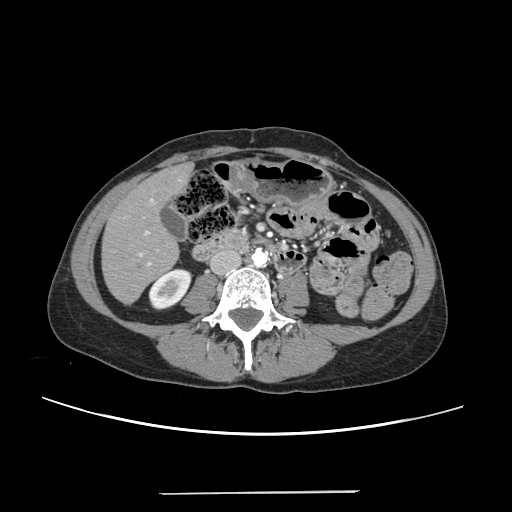
Contrast-enhanced abdominal CT, one axial slice. Position 70 of 240 along the scan axis. 120 kVp. Intravenous contrast given. Soft-tissue window (W 400 / L 40 HU). 1.25 mm slice thickness. 512 × 512 image matrix, field of view 371 × 371 mm. Female patient, age 60 years. Case-level facts recorded for this patient, not image findings: diagnosis: colorectal cancer liver metastases, imaged before liver resection; multiple liver metastases: no.
Annotated regions visible in this slice (manually delineated by an expert):
- liver: bounding box [x1, y1, x2, y2] px = [103, 166, 189, 301]
- planned liver remnant (the part of the liver to remain after resection): [103, 171, 178, 302]
- portal vein (with intrahepatic branches): [139, 198, 158, 265]